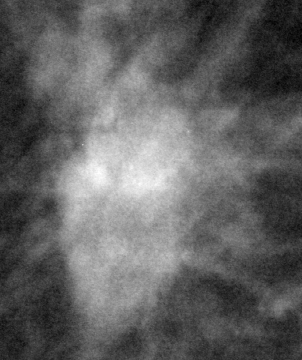
Crop from a digitized film mammogram around one marked abnormality; right breast; MLO view.
- Finding: mass, shape irregular, margins spiculated; BI-RADS assessment category 5; subtlety rating 5 on a 1 (subtle) to 5 (obvious) scale; pathology result (as recorded, not read from the image): malignant.